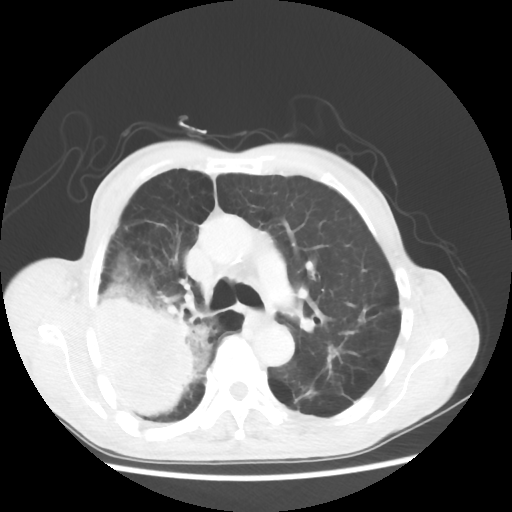
Chest CT, one axial slice. Slice 35 of 58 in the series (ordered by position). 100 kVp. Lung window (W 1500 / L -600 HU). 5 mm slice thickness. 512 × 512 image matrix, field of view 351 × 351 mm. Male patient, age 75 years. Case-level facts recorded for this patient, not image findings: clinical TNM (as recorded): T4 N1 M1.
Structures marked on this image (rectangle marked by the reading radiologist):
- lung tumour (recorded histology: adenocarcinoma): bounding box [x1, y1, x2, y2] px = [91, 269, 213, 418]